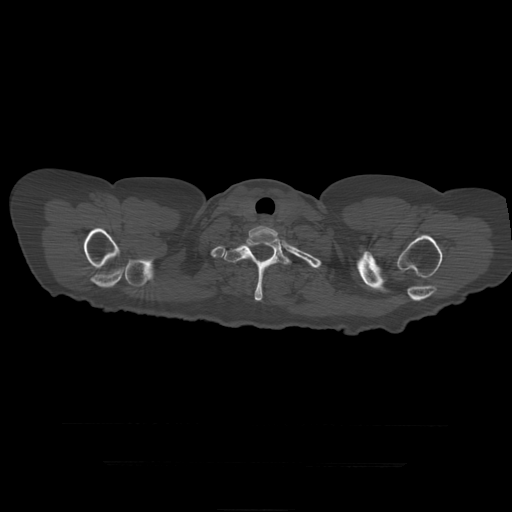
CT including the spine, one axial slice. Position 379 of 399 along the scan axis. Reconstruction kernel STANDARD. 120 kVp. Bone window (W 1800 / L 400 HU). 1.25 mm slice thickness. 512 × 512 image matrix. Patient age 41 years. From the clinical record (not read from this slice): primary cancer: breast.
Outlined on this slice (semi-automatic segmentation, software-assisted and operator-edited):
- T1 vertebra: box from (x=249, y=226) to (x=279, y=261) px
- T2 vertebra: (x=224, y=238)–(x=292, y=301)